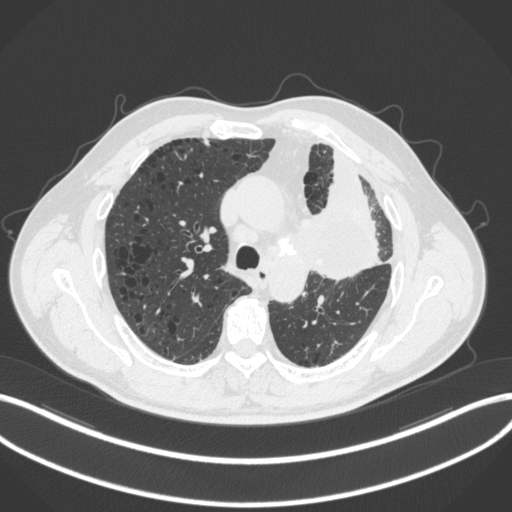
Chest CT, one axial slice; position 201 of 286 along the scan axis; reconstruction kernel B31f; lung window (W 1500 / L -600 HU); 1 mm slice thickness; 512 × 512 image matrix, field of view 400 × 400 mm. Patient: male, 68 years. From the clinical record (not read from this slice): clinical TNM (as recorded): T3 N3 M1.
Annotated regions visible in this slice (bounding box drawn by a radiologist):
- lung tumour (recorded histology: adenocarcinoma): bounding box (x1, y1, x2, y2) in pixels: (294, 176, 387, 285)